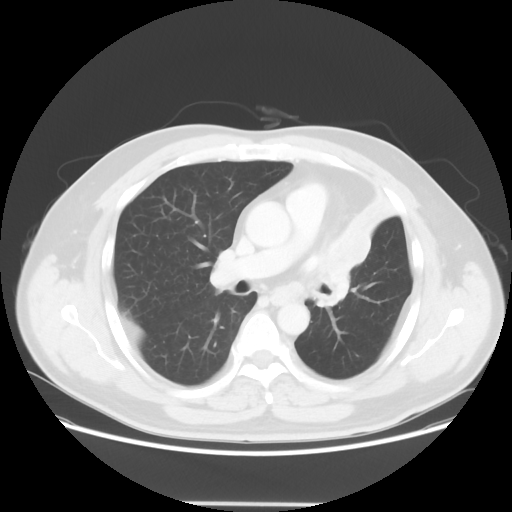
Chest CT, one axial slice. Position 36 of 62 along the scan axis. Reconstruction kernel STANDARD. 120 kVp. Lung window (W 1500 / L -600 HU). 5 mm slice thickness. 512 × 512 image matrix, field of view 403 × 403 mm. Male patient, age 49 years. Case-level facts recorded for this patient, not image findings: clinical TNM (as recorded): T3 N3 M1c.
Annotated regions visible in this slice (bounding box drawn by a radiologist):
- lung tumour (recorded histology: squamous cell carcinoma): bounding box [x1, y1, x2, y2] px = [304, 221, 372, 312]